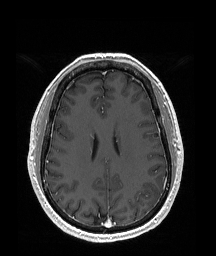
Brain MRI from a brain-tumour surgery series, one axial slice. Slice 77 of 192 in the series (ordered by position). T1-weighted post-contrast. 216 × 256 image matrix. From the clinical record (not read from this slice): histopathology: Glioblastoma; WHO grade: 4; IDH mutation: no; tumour location: Left Temporal Parietal.
Outlined on this slice (outlined manually by an expert reader):
- tumour: bounding box (x1, y1, x2, y2) in pixels: (142, 182, 163, 208)